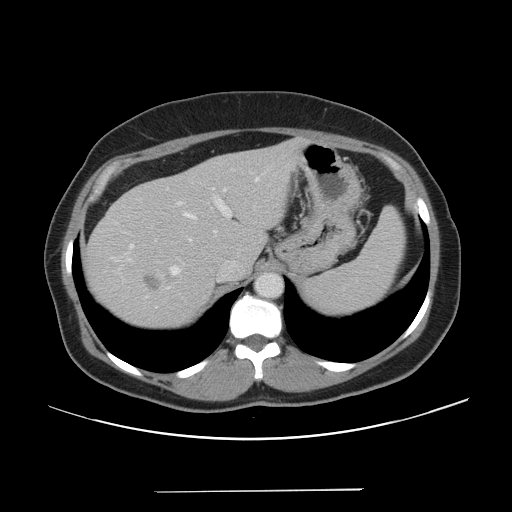
Contrast-enhanced abdominal CT, one axial slice. Position 34 of 56 along the scan axis. 120 kVp. Soft-tissue window (W 400 / L 40 HU). 512 × 512 image matrix, field of view 419 × 419 mm. Female patient, age 54 years. From the clinical record (not read from this slice): diagnosis: colorectal cancer liver metastases, imaged before liver resection; multiple liver metastases: yes; largest metastasis: 3.2 cm; disease in both lobes: yes.
Structures marked on this image (expert manual segmentation):
- hepatic veins: box from (x=119, y=177) to (x=260, y=277) px
- liver: (x=84, y=138)–(x=306, y=332)
- planned liver remnant (the part of the liver to remain after resection): (x=184, y=138)–(x=308, y=268)
- portal vein (with intrahepatic branches): (x=210, y=187)–(x=232, y=219)
- liver metastasis: (x=144, y=268)–(x=170, y=291)